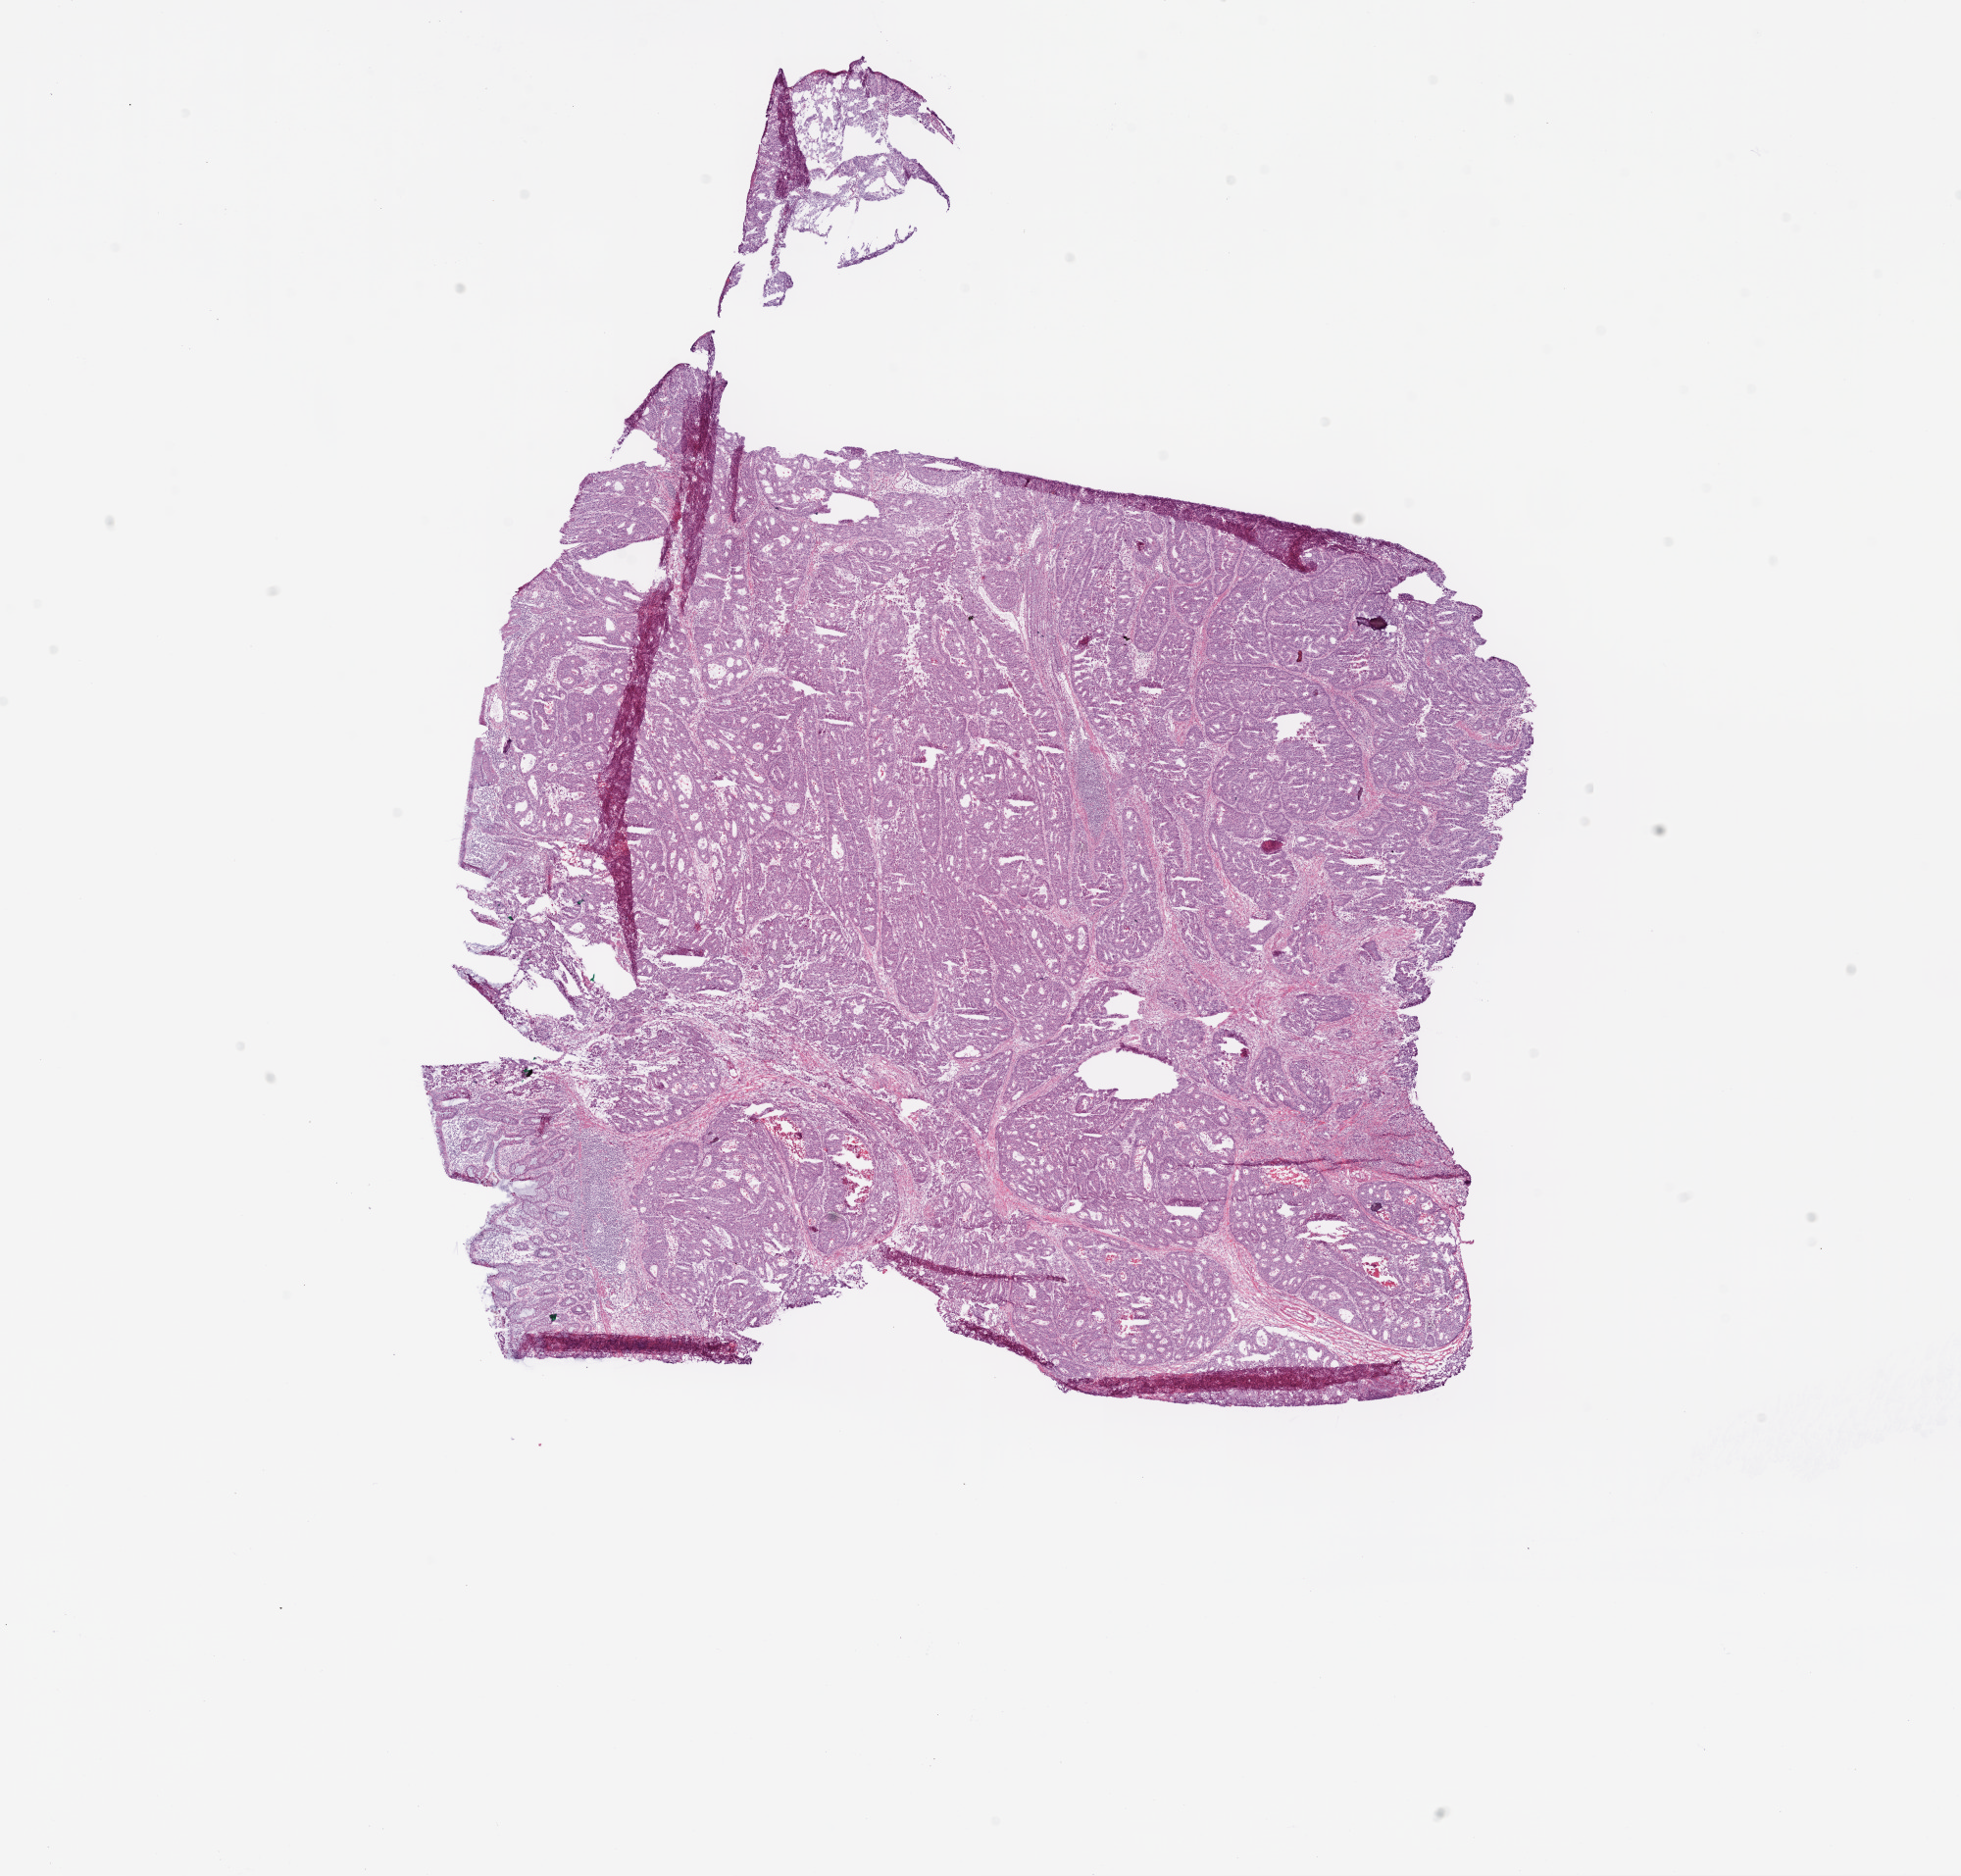
Whole-slide histology image, H&E, whole scanned area (about 16.0 x 15.4 mm) shown as a low-resolution overview, frozen section from the bottom of the tissue portion, sample: primary tumour, colon. Female, age 82 years at initial diagnosis. Slide review estimates, as recorded: tumour cells 77%, tumour nuclei 85%, normal cells 5%, stromal cells 10%, necrosis 8%.
TNM: T3 N2 M0. Lymph nodes positive (case pathology): 6 of 12 examined. Pathologic diagnosis: Adenocarcinoma, NOS. AJCC pathologic stage: IIIC (6th edition).